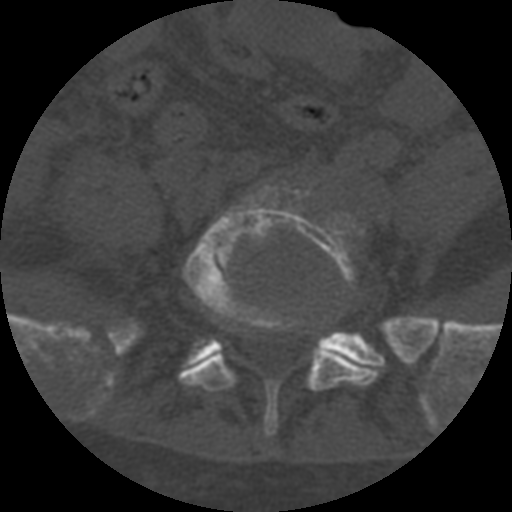
CT including the spine, one axial slice. Slice 178 of 708 in the series (ordered by position). 120 kVp. One of 3 acquisitions stored at this slice position. Bone window (W 1800 / L 400 HU). 1.25 mm slice thickness. 512 × 512 image matrix, field of view 160 × 160 mm. Patient age 55 years. From the clinical record (not read from this slice): primary cancer: colon.
Annotated regions visible in this slice (semi-automatically segmented with operator editing):
- L5 vertebra: box from (x=178, y=185) to (x=381, y=436) px